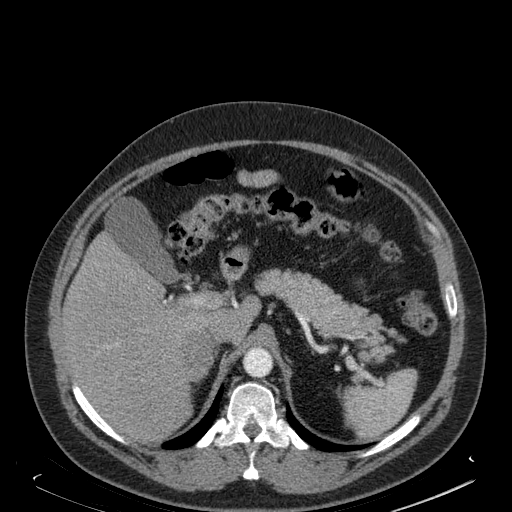
Contrast-enhanced abdominal CT, one axial slice; position 127 of 181 along the scan axis; soft-tissue window (W 400 / L 40 HU); 1.5 mm slice thickness; 512 × 512 image matrix. Male patient. Case-level facts recorded for this patient, not image findings: diagnosis: adrenocortical carcinoma; tumour side: right adrenal.
Annotated regions visible in this slice (semi-automatic segmentation, software-assisted and operator-edited):
- mass: bounding box <183,330,214,380> (left, top, right, bottom; pixels)